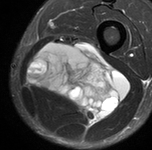
MRI of an extremity soft-tissue mass, one axial slice. Slice 40 of 90 in the series (ordered by position). STIR. MR volume resampled by the dataset authors to the PET/CT grid (not the native acquisition matrix). 152 × 150 image matrix, field of view 148 × 146 mm. Male patient. From the clinical record (not read from this slice): histological type: undifferentiated pleomorphic liposarcoma; grade: high; site of the primary tumour: left thigh.
Outlined on this slice (expert contour drawn on MRI and transferred to this co-registered scan by the dataset authors):
- gross tumour volume including surrounding oedema: bounding box (x1, y1, x2, y2) in pixels: (29, 39, 129, 124)
- gross tumour volume (mass): (29, 44, 129, 124)